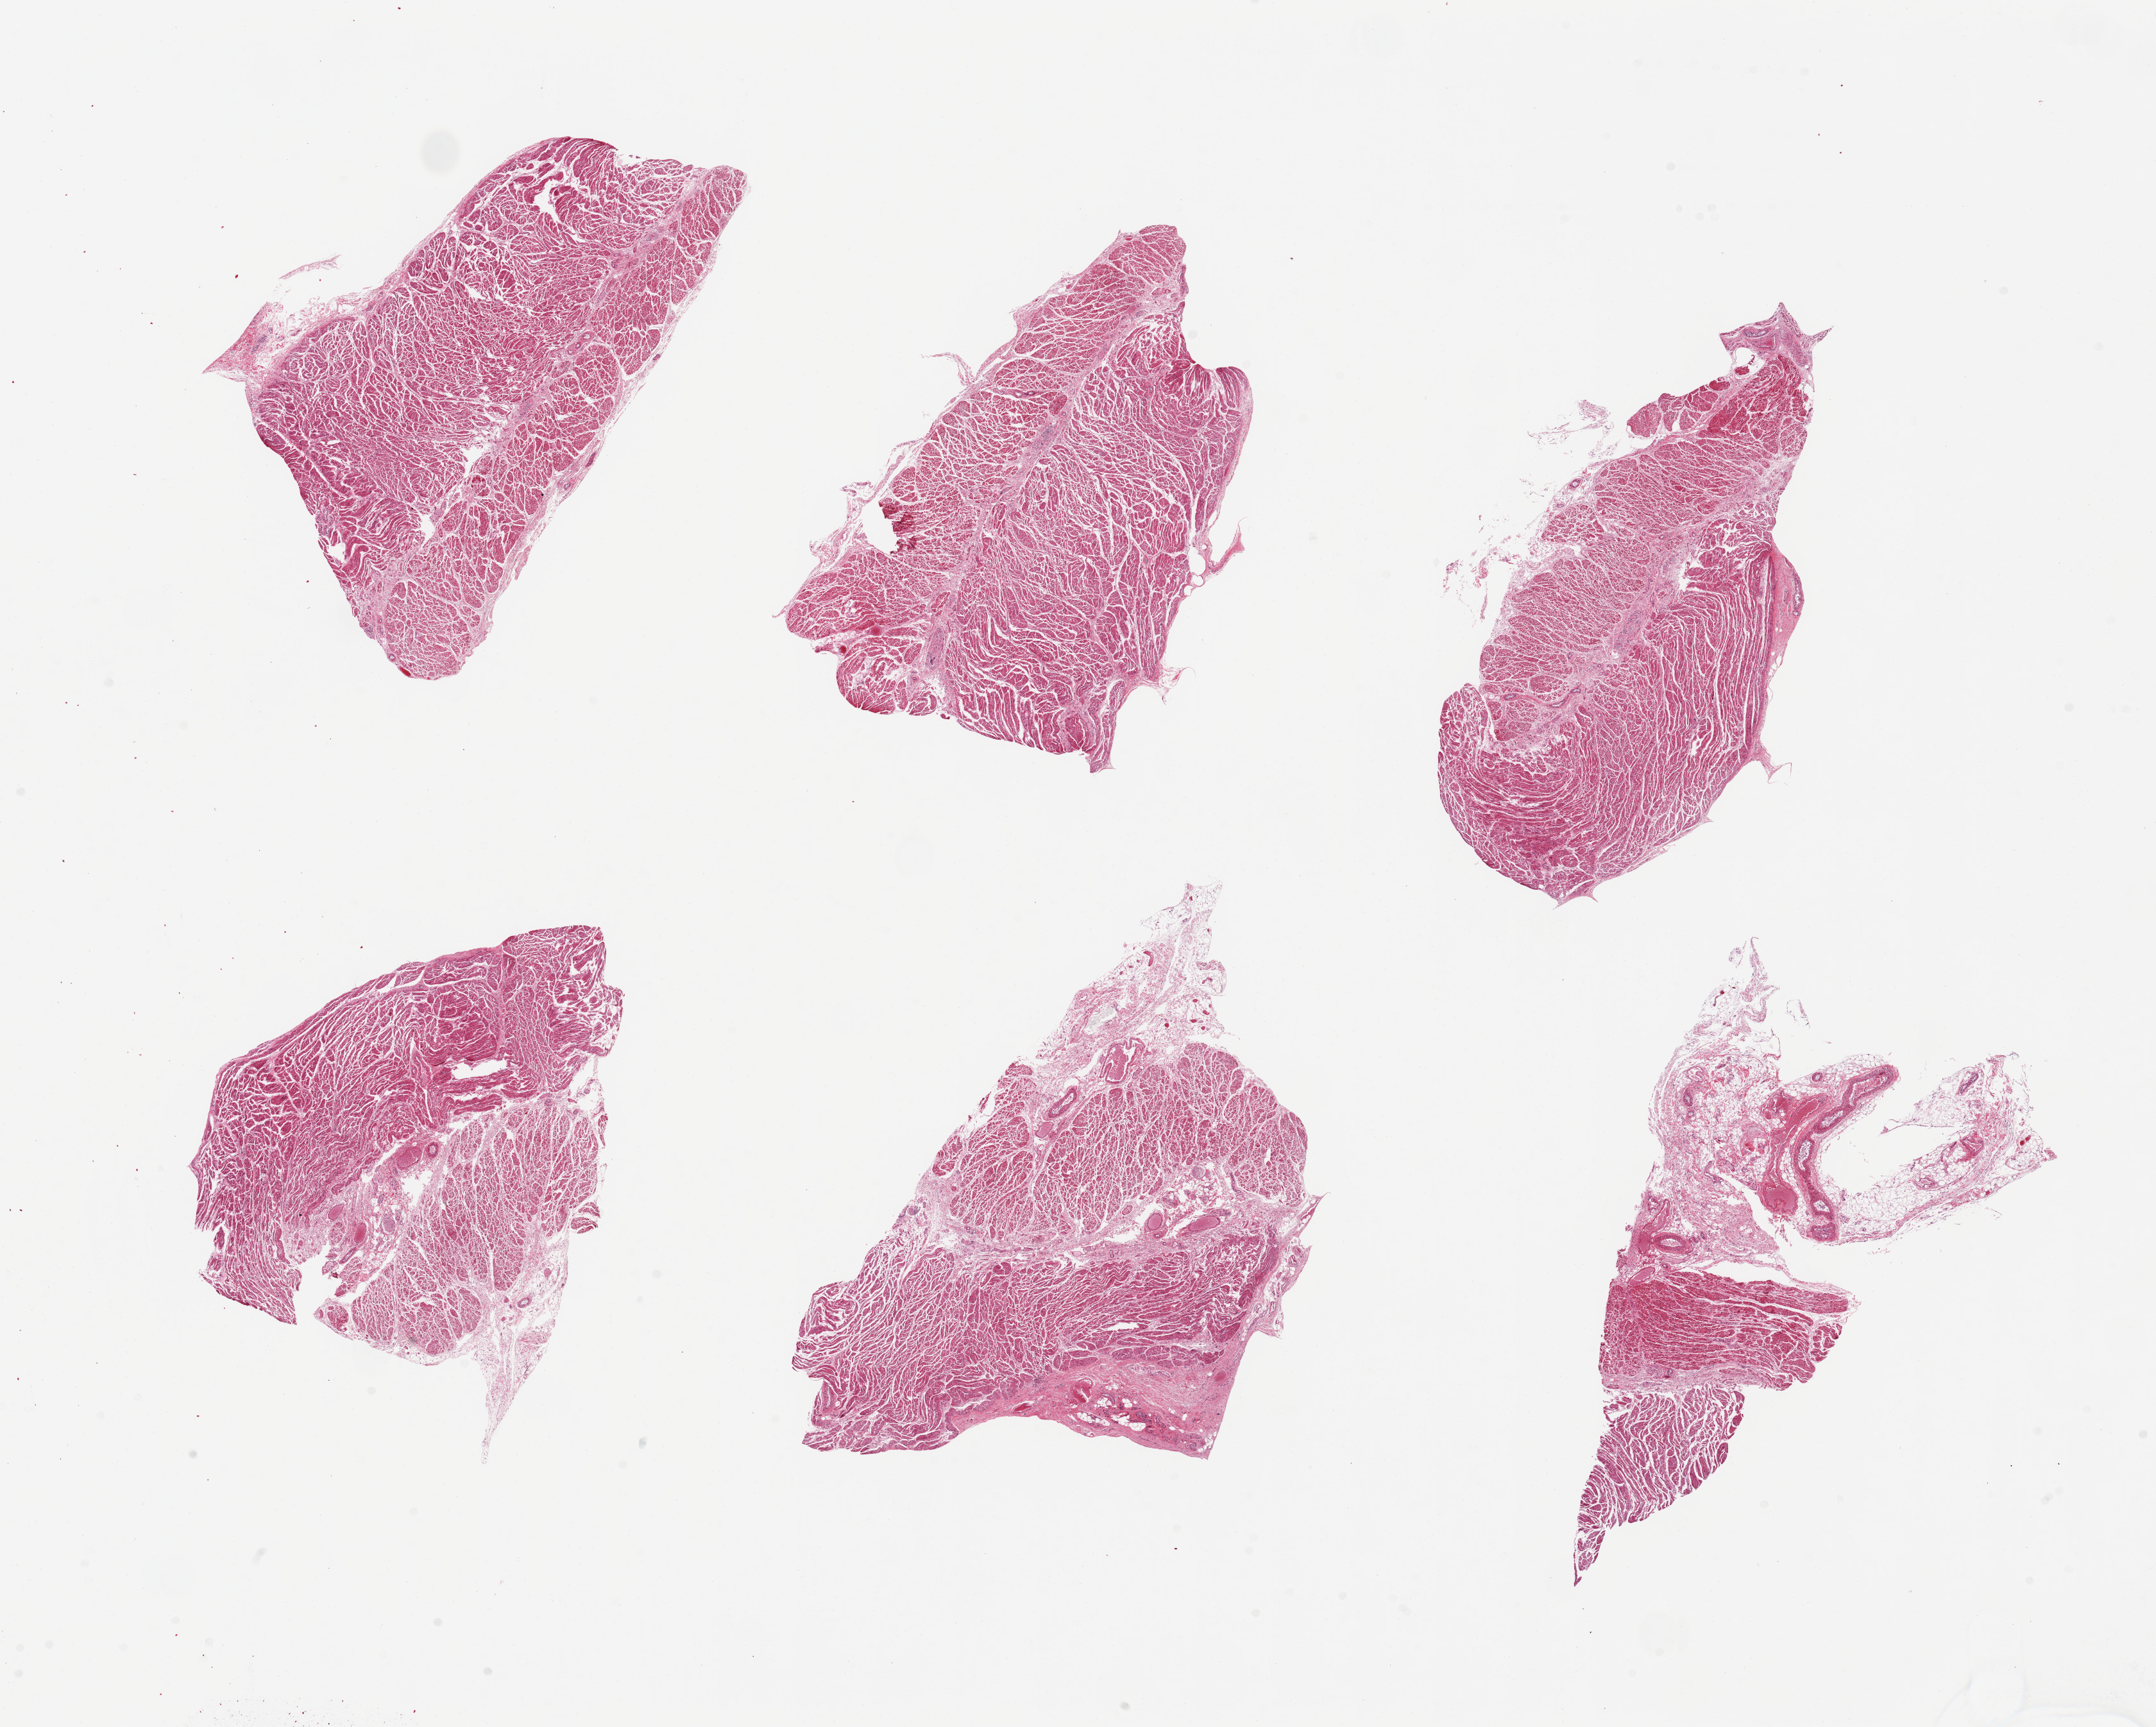
H&E whole-slide image — whole scanned area (about 26.6 x 21.3 mm) shown as a low-resolution overview. PAXgene-fixed, paraffin-embedded tissue. Section of gastroesophageal junction (target tissue). Donor tissue sample. Donor: male.
Pathologist's review note for this sample: 6 pieces, up to 8.5x5mm; all muscle except smallest piece is 60% fibroadipose.